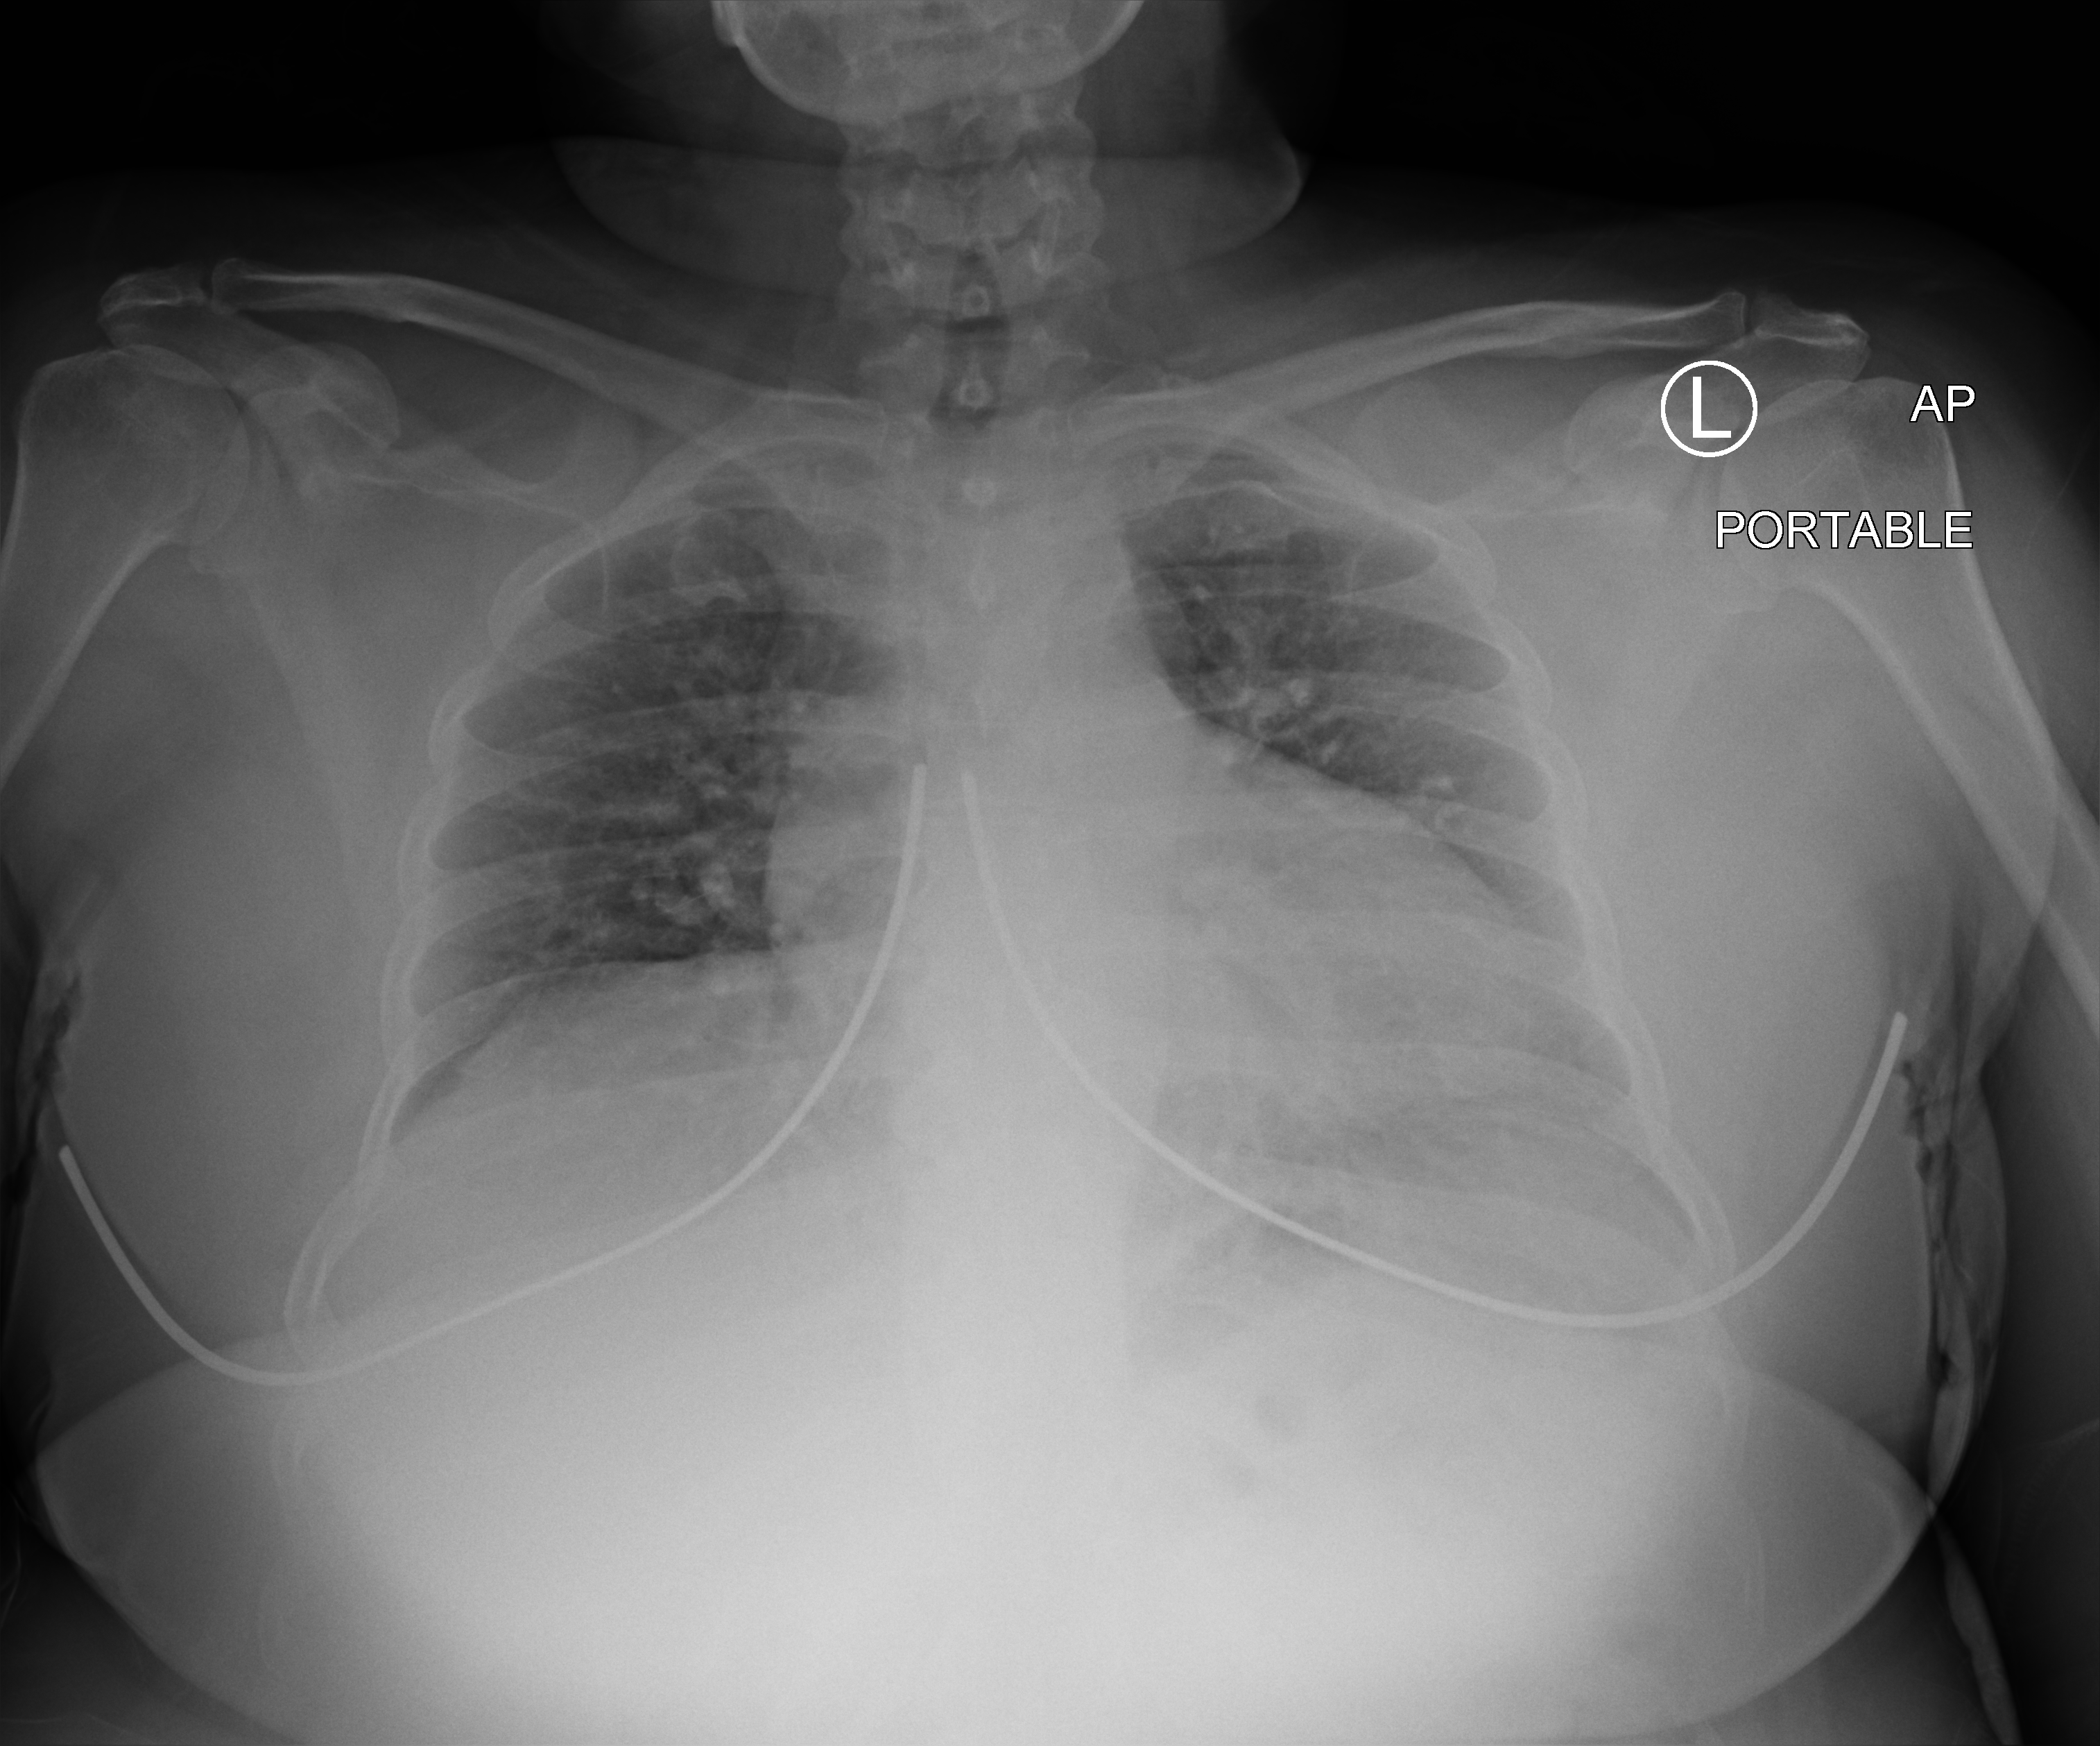
Portable chest radiograph; anteroposterior (AP) projection. Patient hospitalised with COVID-19; female, aged 18–59 years.
From the hospital-stay record, not from the radiograph (when in the stay this image was taken is not recorded): length of hospital stay: 2 days; admitted to intensive care during this hospital stay: no; mechanically ventilated during this hospital stay: no.